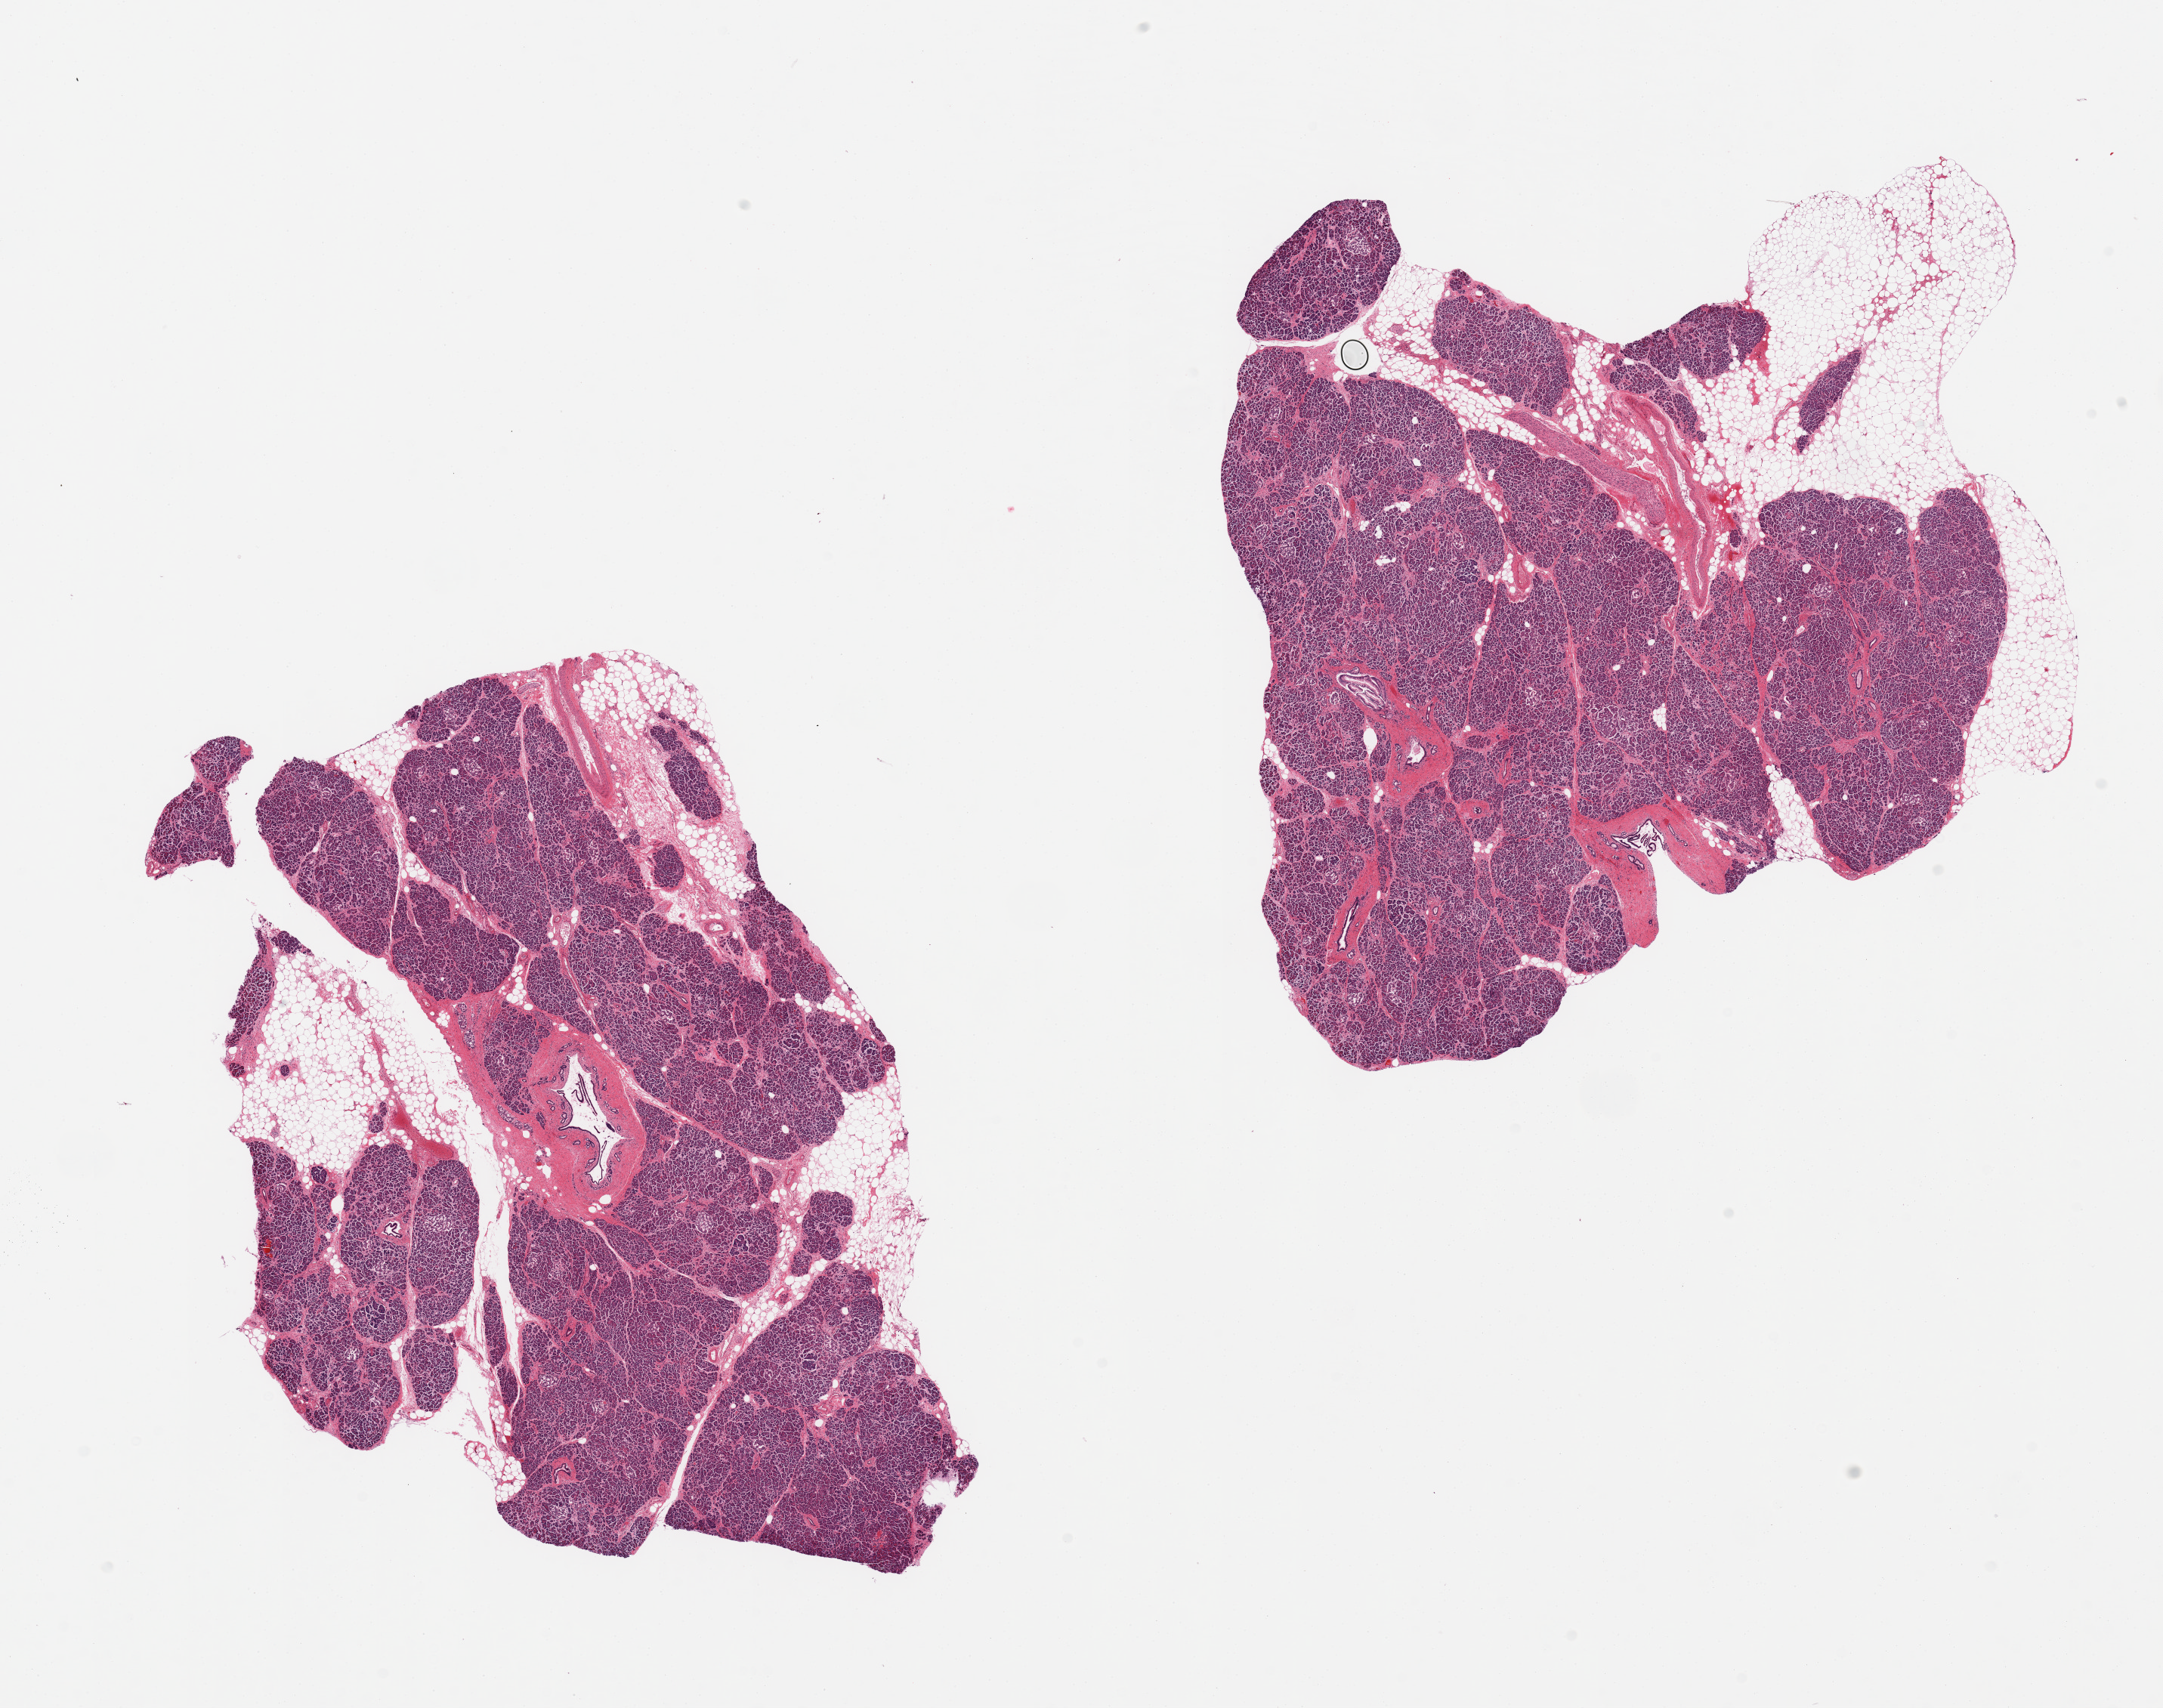
Digitized H&E-stained section — a low-resolution overview of the entire scanned area, about 22.6 x 17.9 mm (slide scanned at 20x); PAXgene-fixed, paraffin-embedded tissue; target tissue: pancreas; donor tissue sample. Donor sex: female.
Review note (as recorded): 2 pieces; 30% external fat.